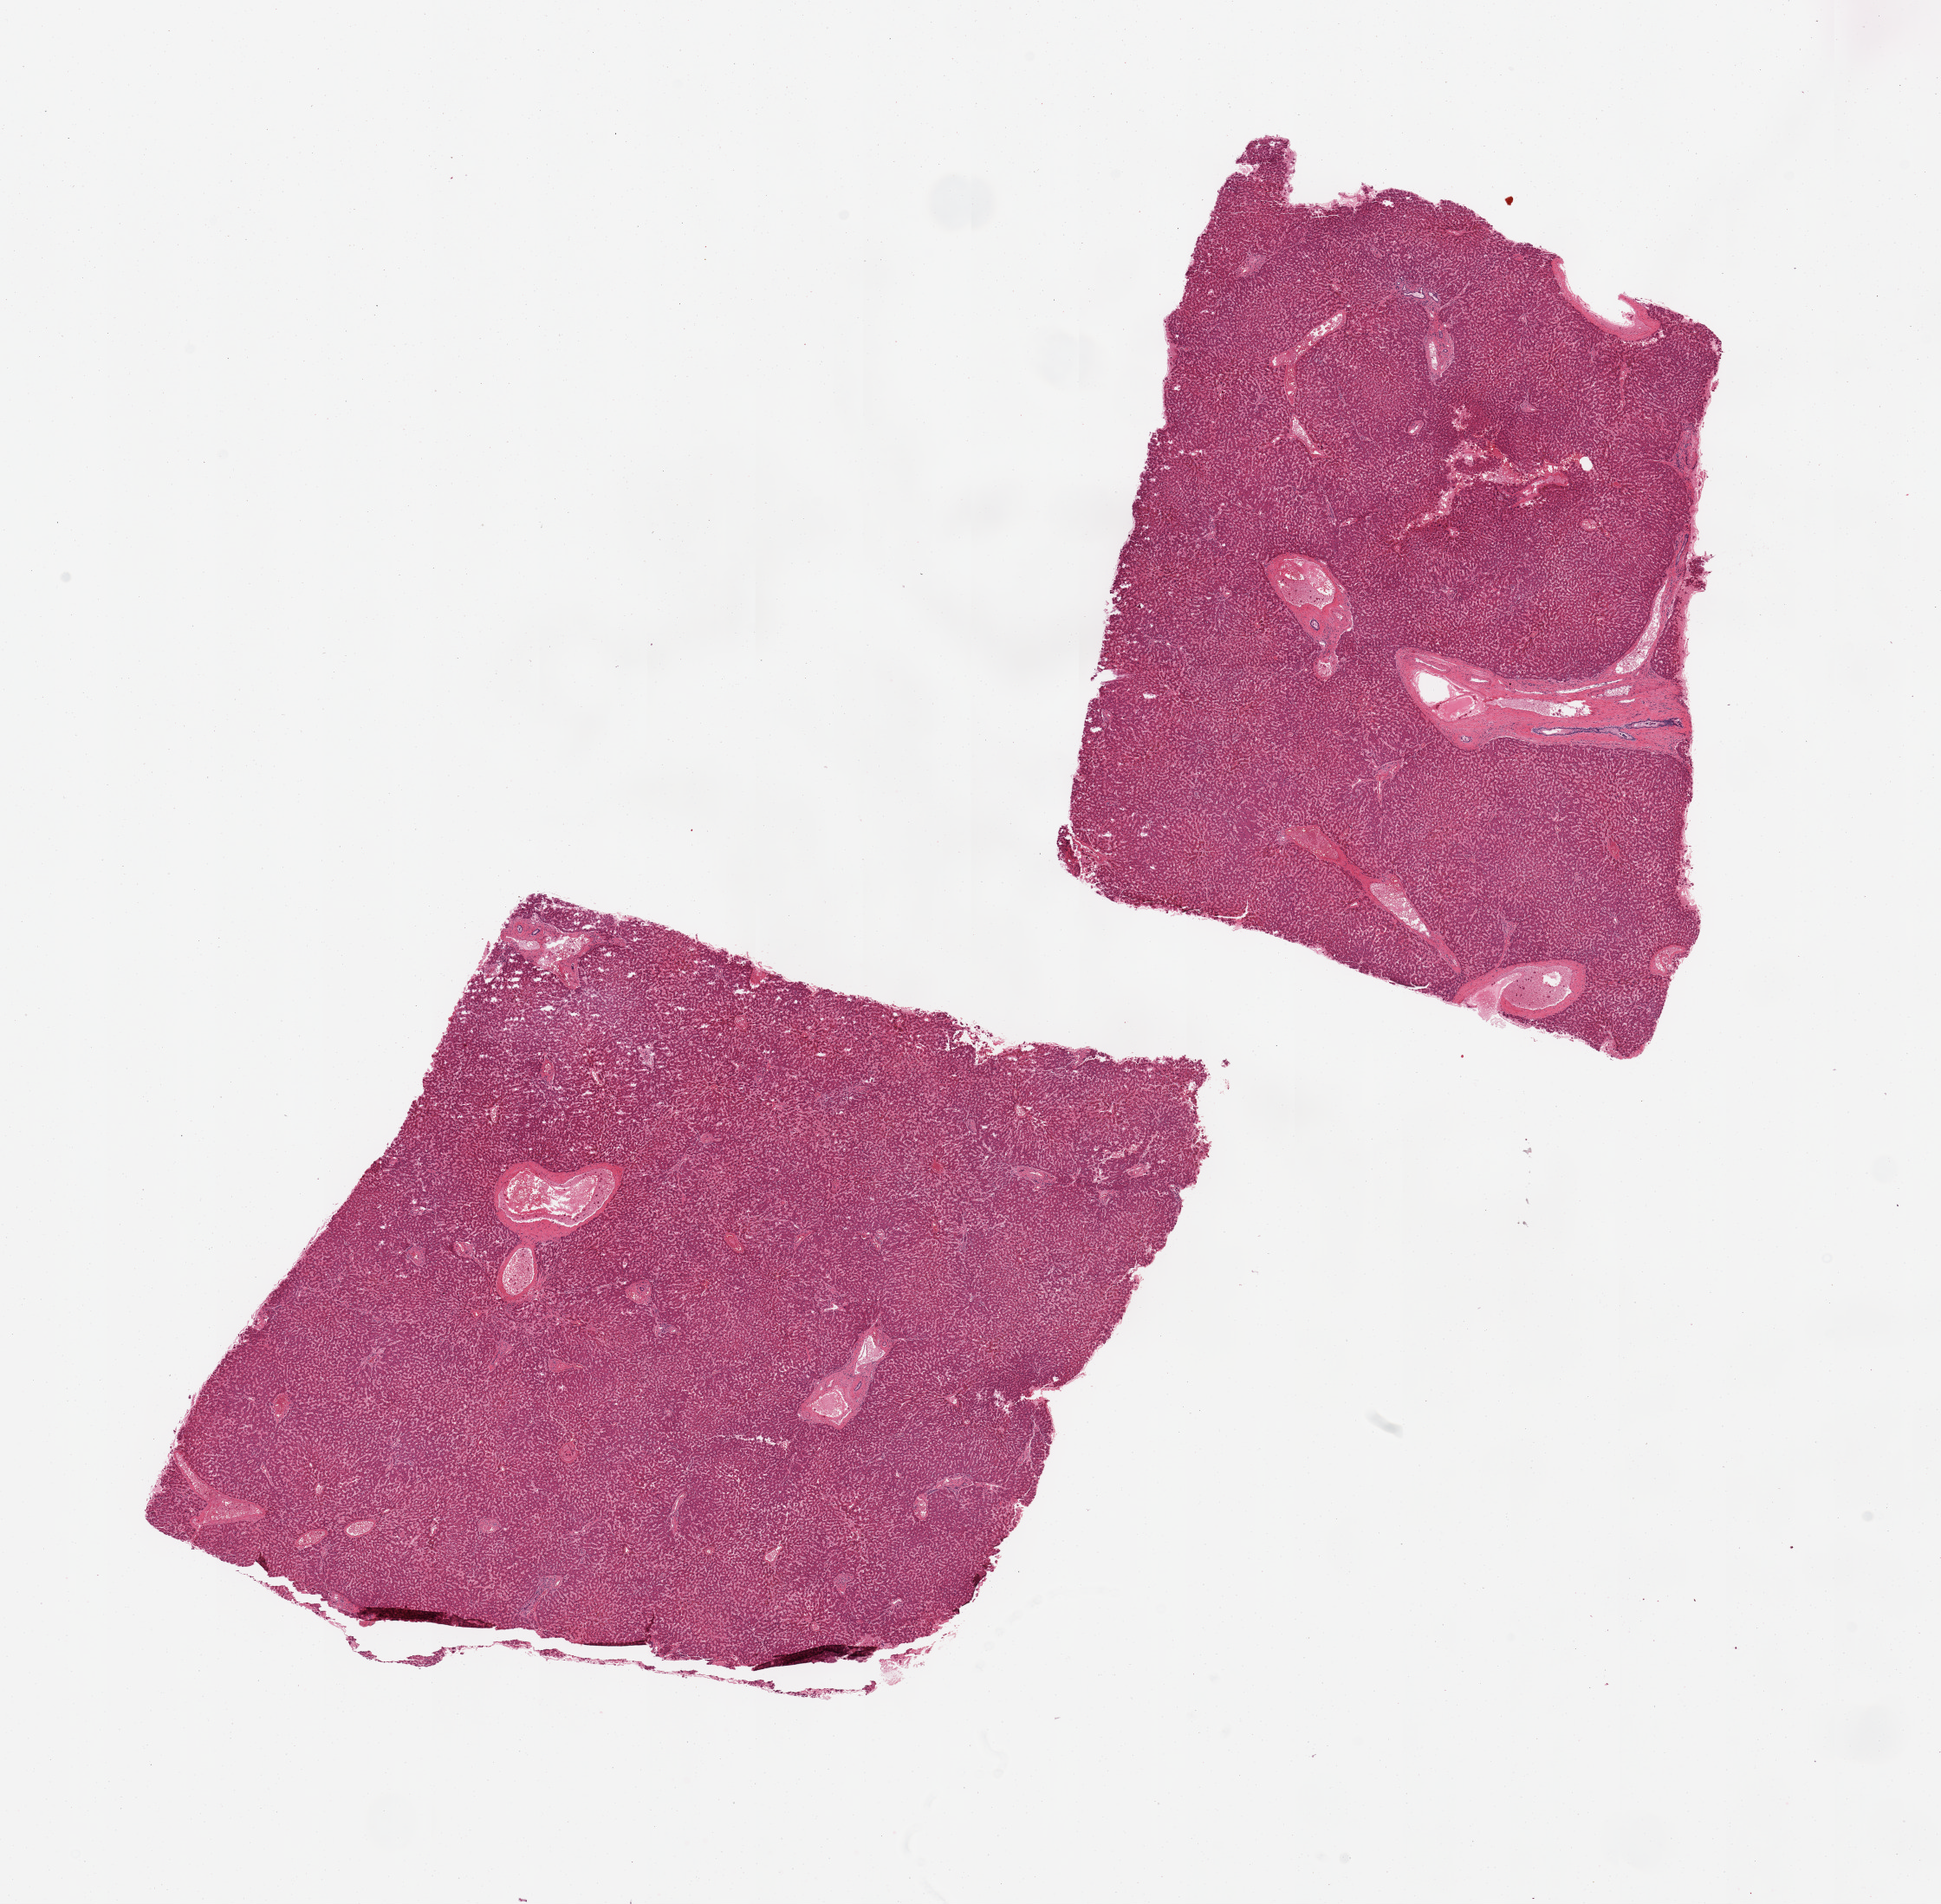
Hematoxylin and eosin (H&E) whole-slide image — a low-resolution overview of the entire scanned area, about 17.7 x 17.4 mm (acquisition: 20x scan). PAXgene-fixed, paraffin-embedded tissue. Sampled site (target tissue): liver. Tissue donor sample.
Review note (as recorded): 2 pieces moderate congestion; no significant steatosis or hepatitis noted.